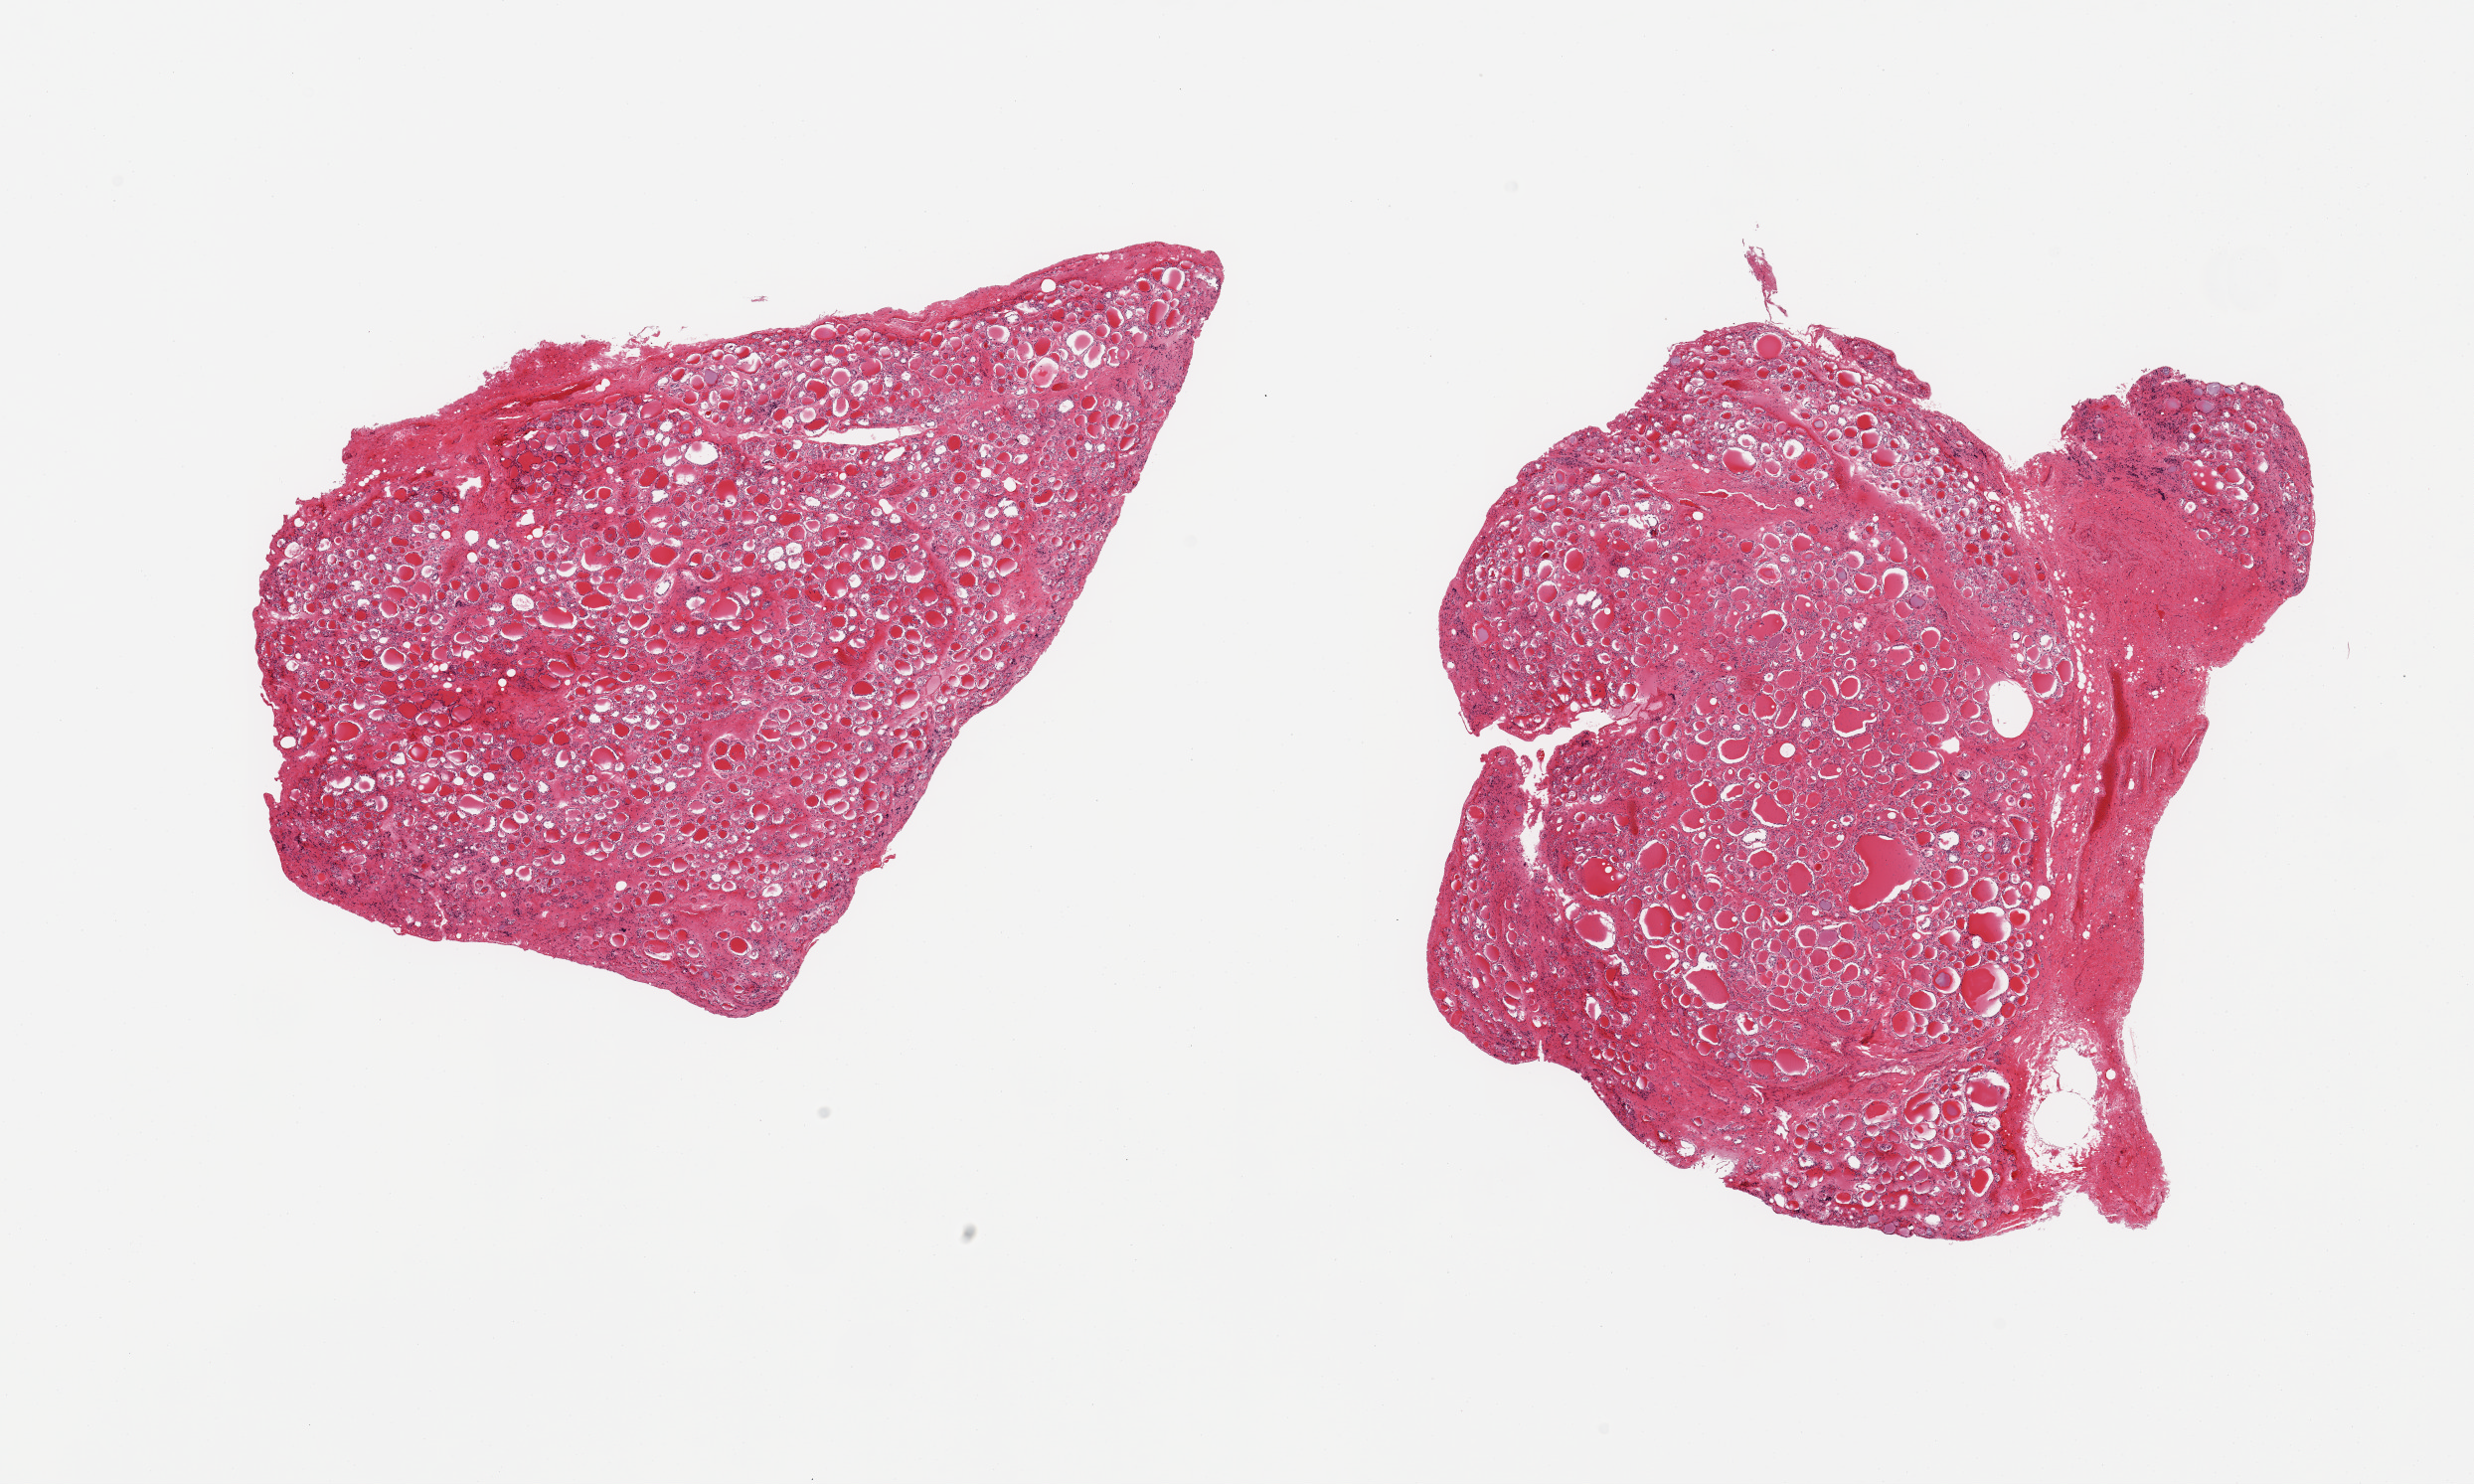
H&E whole-slide image, low-resolution overview of the scanned area, about 19.7 x 11.8 mm, PAXgene-fixed, paraffin-embedded tissue, sampled site (target tissue): thyroid, donor tissue sample. Donor: female.
Reviewer comment on this tissue sample: 2 pieces; mild interstitial fibrosis and nodularity.